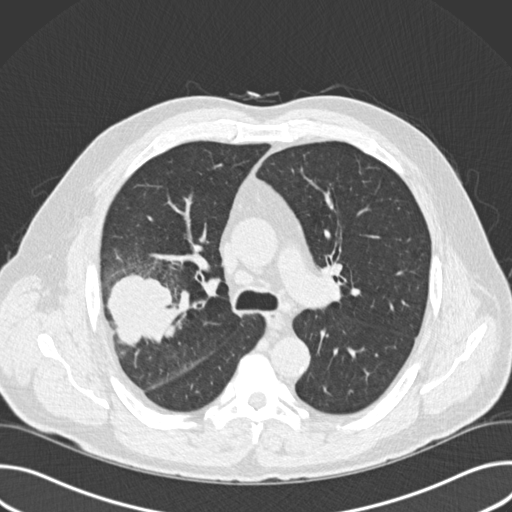
Low-dose screening chest CT, one axial slice. Slice 105 of 157 in the series (ordered by position). Reconstruction kernel B30f. Lung window (W 1500 / L -600 HU). 512 × 512 image matrix, field of view 380 × 380 mm.
Annotated regions visible in this slice (expert manual segmentation):
- lesion 1 (tumor, upper lobe of right lung): bounding box <107,274,180,346> (left, top, right, bottom; pixels)